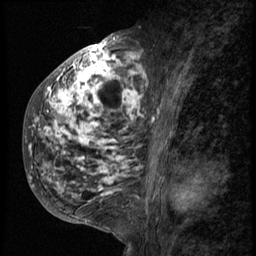
Breast MRI (dynamic contrast-enhanced), one sagittal slice. Slice 29 of 58 in the series (ordered by position). 3 images stored at this slice position (order not interpretable as contrast timing). 1.5 T. TE 4.2 ms, TR 9 ms. 2.5 mm slice thickness. 256 × 256 image matrix, field of view 180 × 180 mm. Patient: female, 50 years. From the clinical record (not read from this slice): setting: breast cancer imaged before/during neoadjuvant chemotherapy; receptor status: triple-negative.
Outlined on this slice (semi-automatically segmented with operator editing):
- analysis volume of interest (the breast-tissue region the enhancement analysis was run in; not a lesion): bounding box [x1, y1, x2, y2] px = [24, 48, 153, 214]
- tumour enhancement mask (voxels above the 140 % enhancement threshold inside the analysis volume of interest): [30, 48, 151, 199]